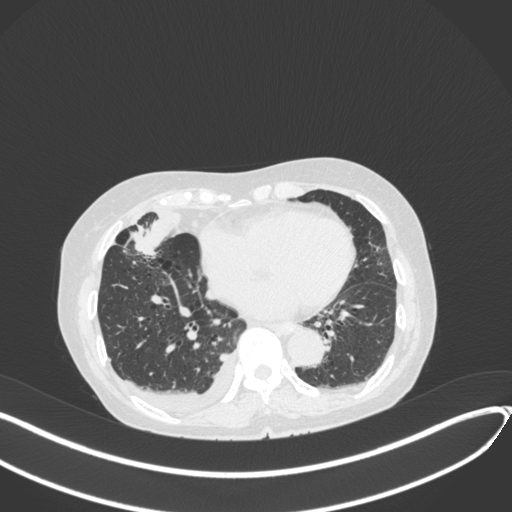
Chest CT, one axial slice; slice 139 of 418 in the series (ordered by position); reconstruction kernel B31f; 120 kVp; lung window (W 1500 / L -600 HU); 1 mm slice thickness; 512 × 512 image matrix. Patient: female, 75 years. From the clinical record (not read from this slice): clinical TNM (as recorded): T2a N3 M0.
Annotated regions visible in this slice (bounding box drawn by a radiologist):
- lung tumour (recorded histology: adenocarcinoma): box from (x=126, y=214) to (x=190, y=263) px